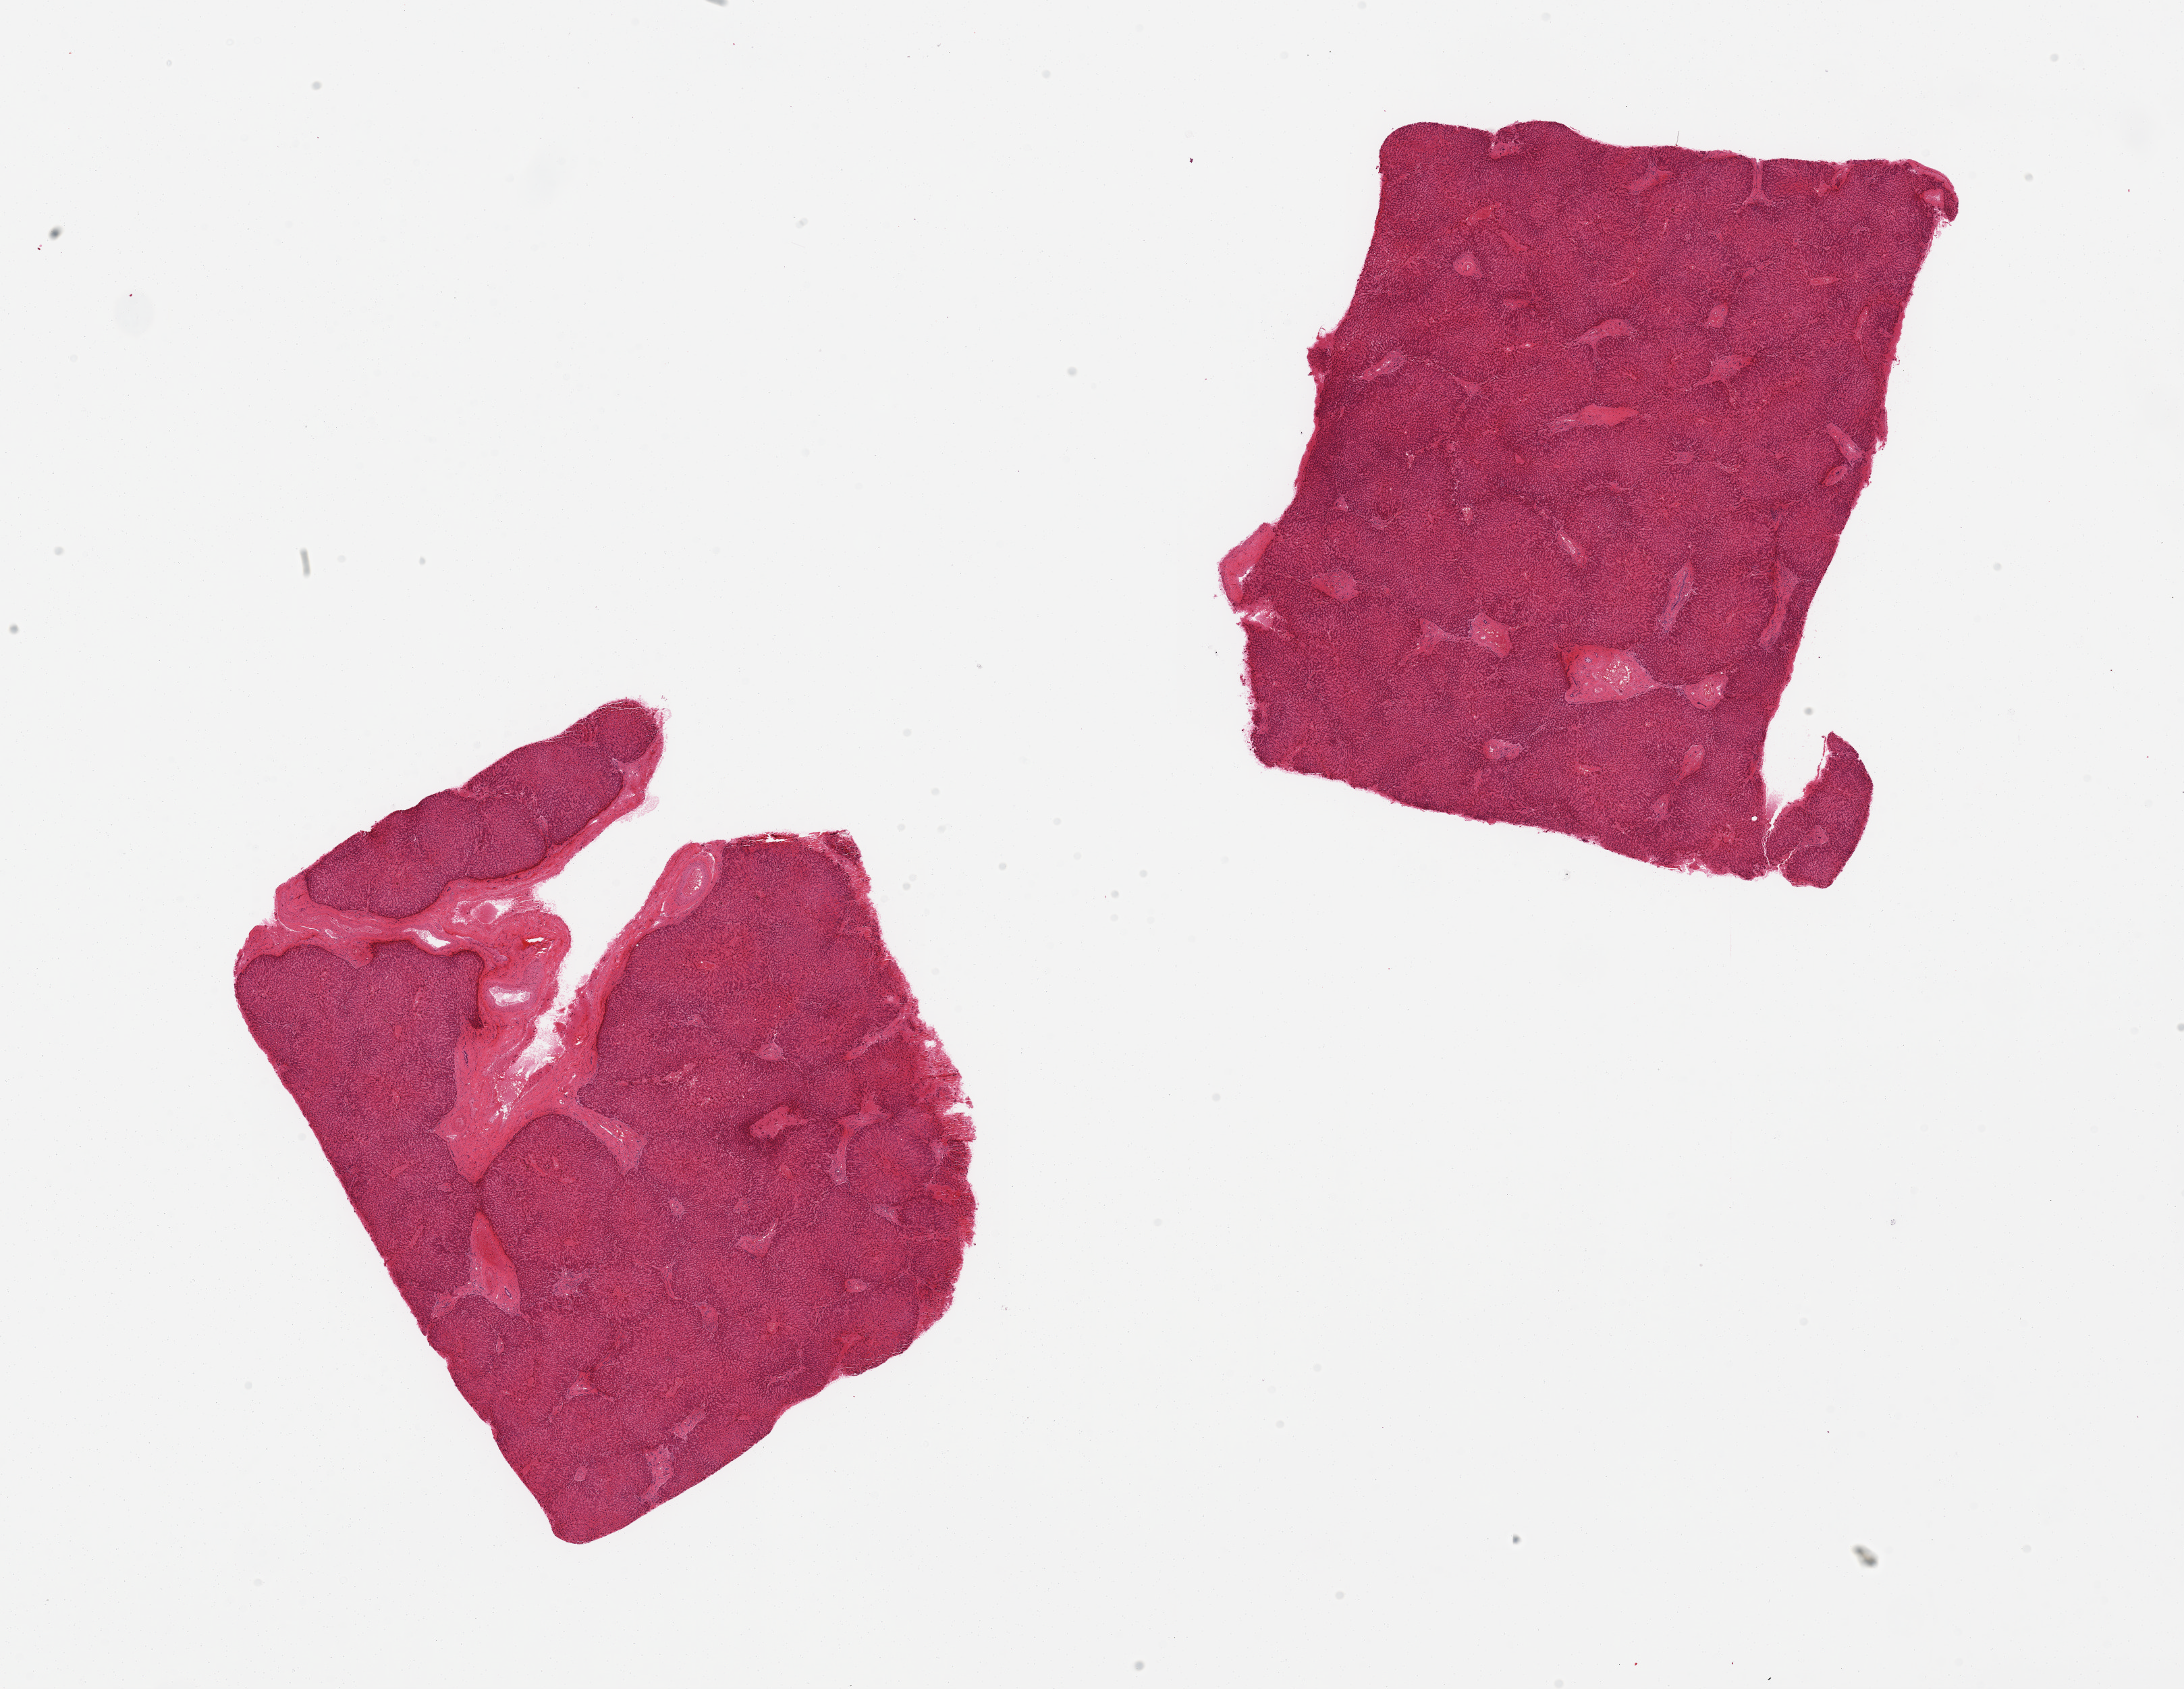
Hematoxylin and eosin (H&E) whole-slide image — whole scanned area (about 25.6 x 19.8 mm, acquisition: 20x scan) shown as a low-resolution overview; PAXgene-fixed, paraffin-embedded tissue; target tissue: liver; donor tissue sample. Donor: male.
Review note (as recorded): 2 pieces, moderate-marked chronic passive congestion ('nutmeg' changes).